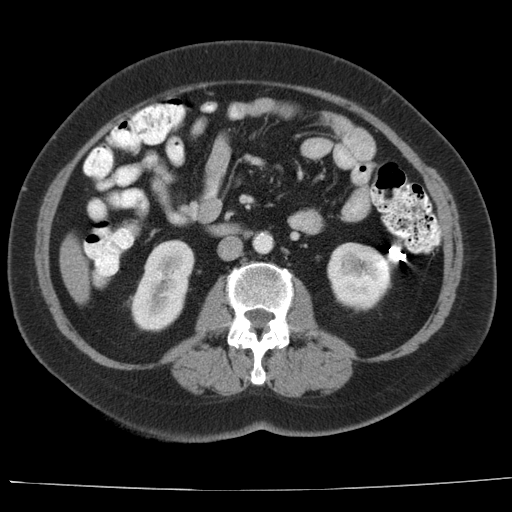
Contrast-enhanced abdominal CT, one axial slice; slice 3 of 44 in the series (ordered by position); 140 kVp; intravenous contrast given; soft-tissue window (W 400 / L 40 HU); 5 mm slice thickness; 512 × 512 image matrix, field of view 373 × 373 mm. Female patient. Case-level facts recorded for this patient, not image findings: diagnosis: colorectal cancer liver metastases, imaged before liver resection; multiple liver metastases: yes; largest metastasis: 1.8 cm; disease in both lobes: no.
Annotated regions visible in this slice (manually delineated by an expert):
- liver: box from (x=61, y=238) to (x=91, y=302) px